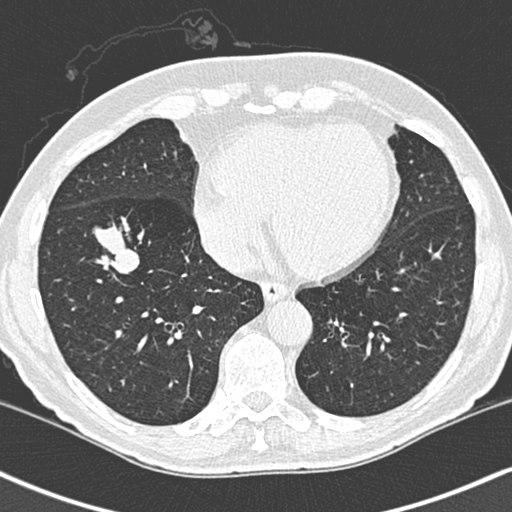
Low-dose screening chest CT, one axial slice; position 93 of 248 along the scan axis; 120 kVp; lung window (W 1500 / L -600 HU); 1.3 mm slice thickness; 512 × 512 image matrix, field of view 323 × 323 mm.
Annotated regions visible in this slice (expert manual segmentation):
- lesion 1 (tumor, lower lobe of right lung): bounding box (x1, y1, x2, y2) in pixels: (93, 185, 140, 236)